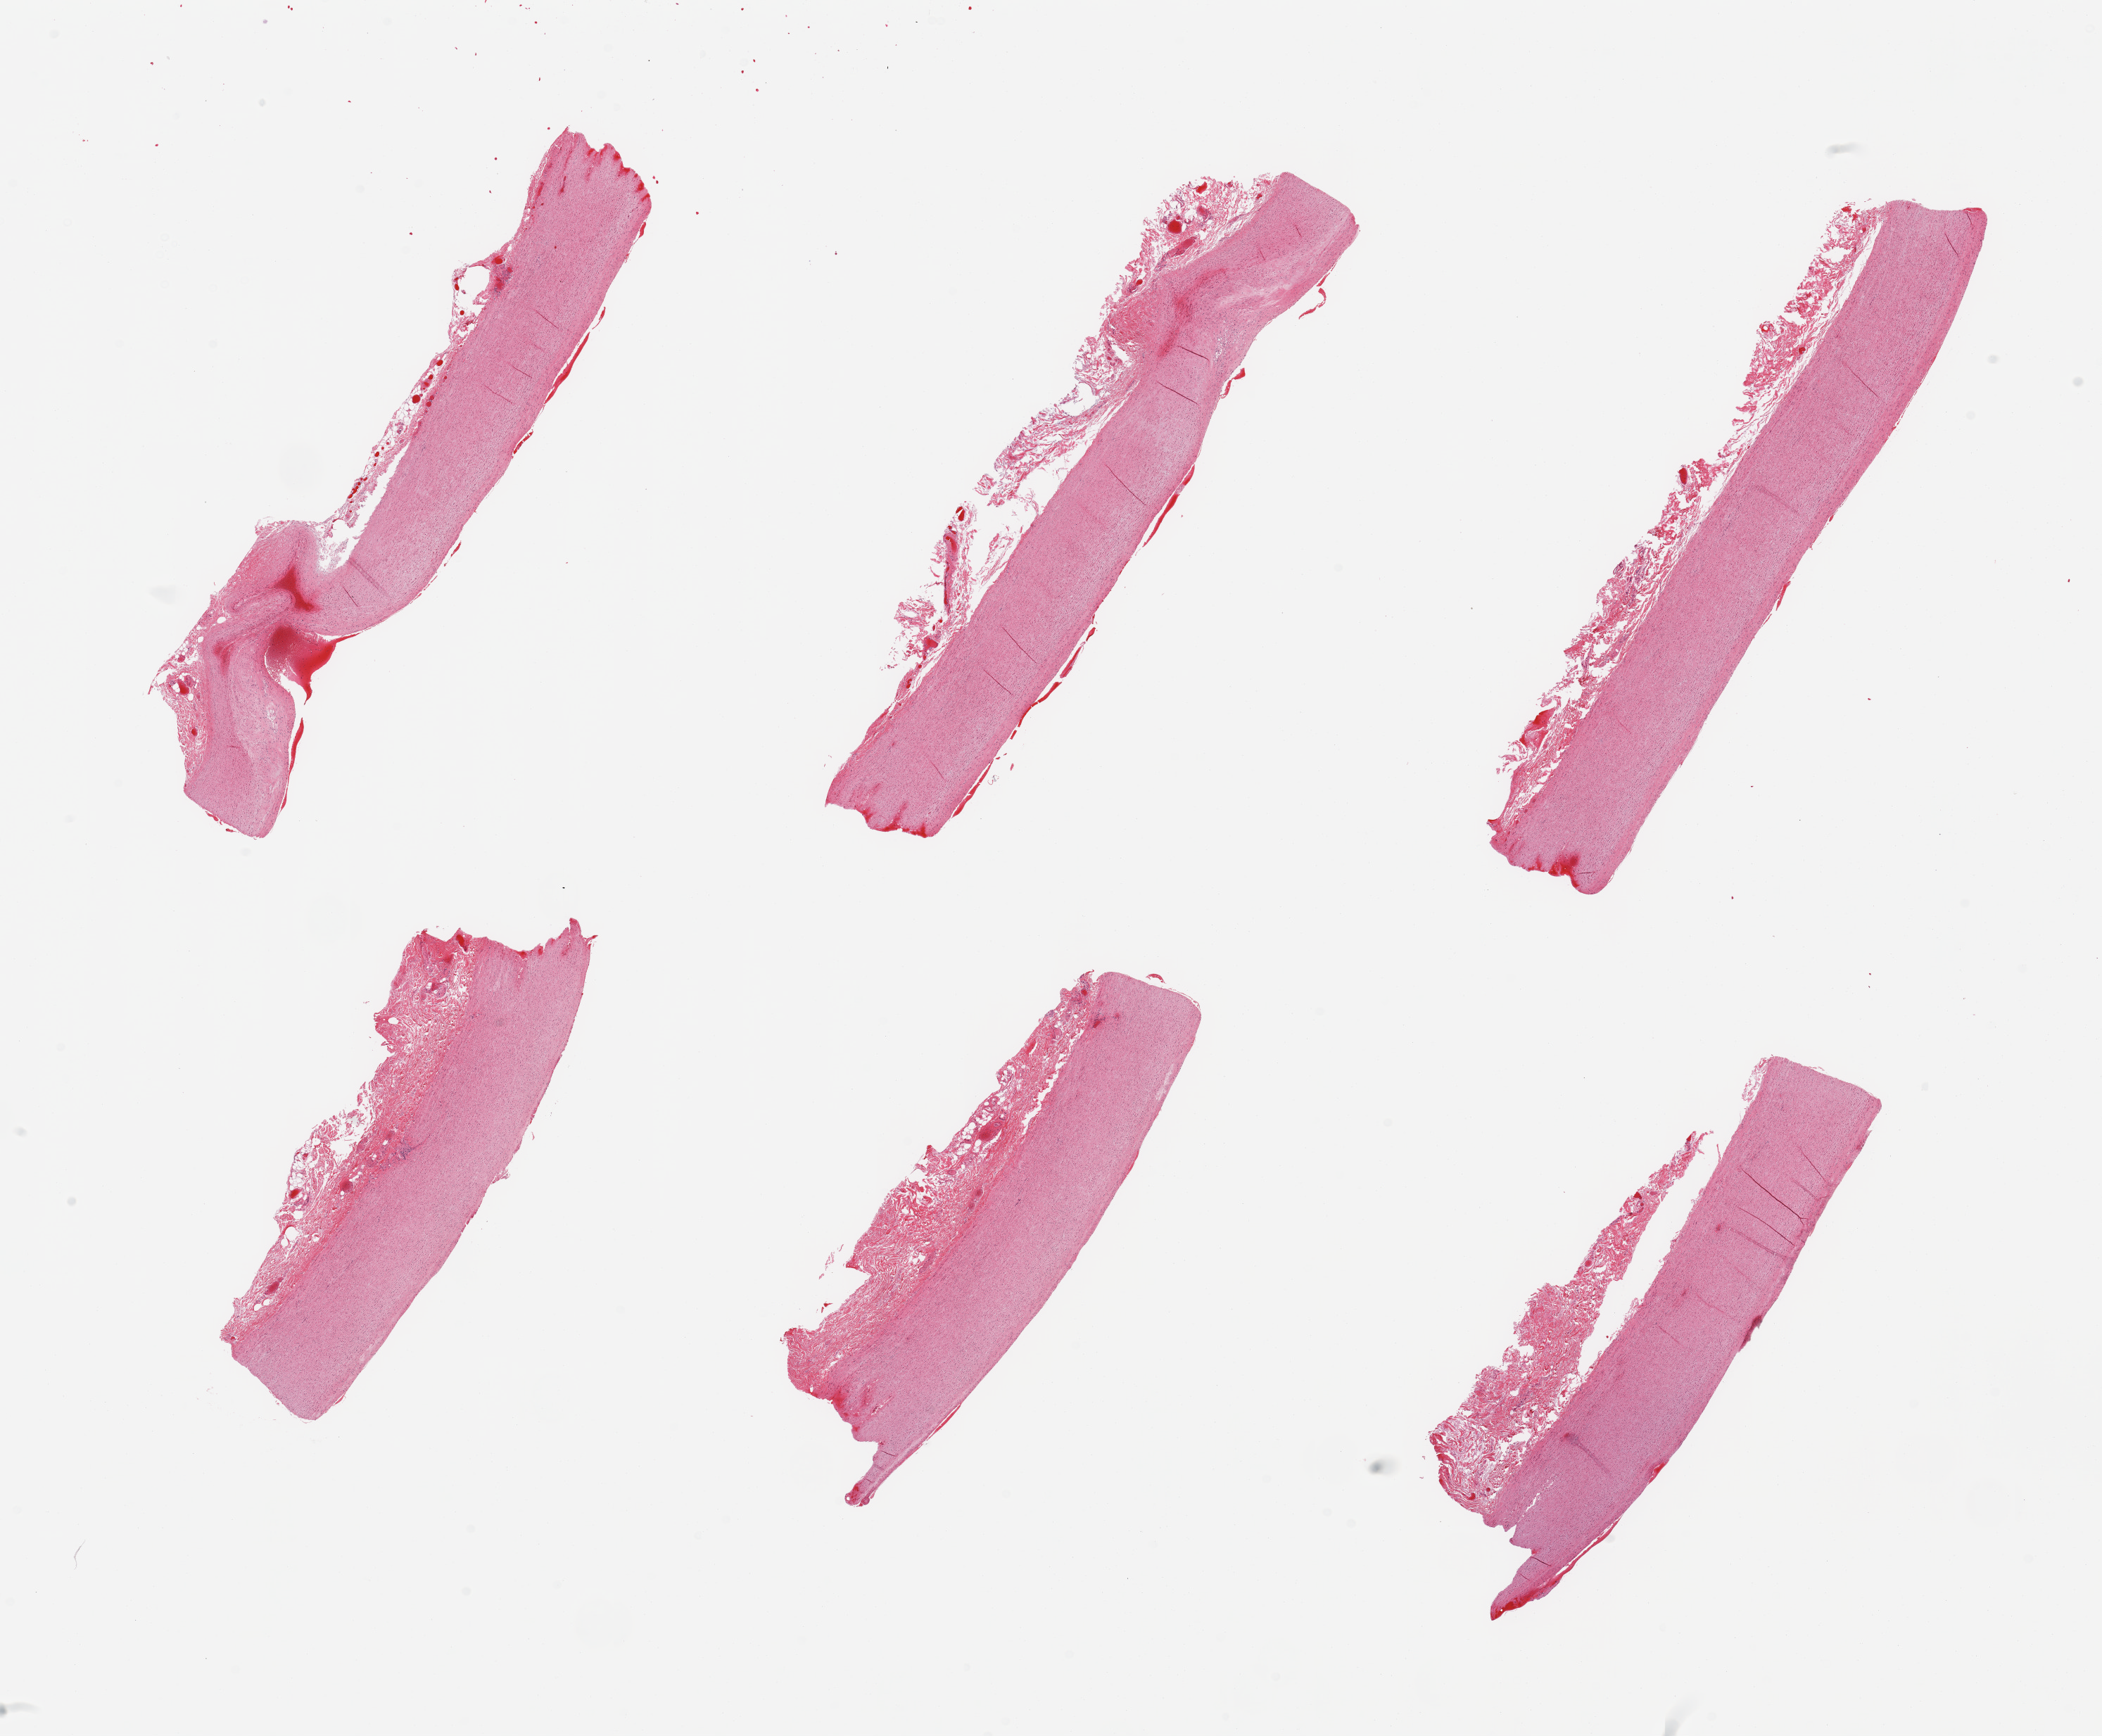
Haematoxylin and eosin whole-slide image, brightfield — whole scanned area (about 23.6 x 19.5 mm, from a 20x scan) shown as a low-resolution overview, PAXgene-fixed, paraffin-embedded tissue, target tissue: aorta, donor tissue sample. Donor: female.
Review note (as recorded): 6 pieces; minimal plaque; well trimmed.